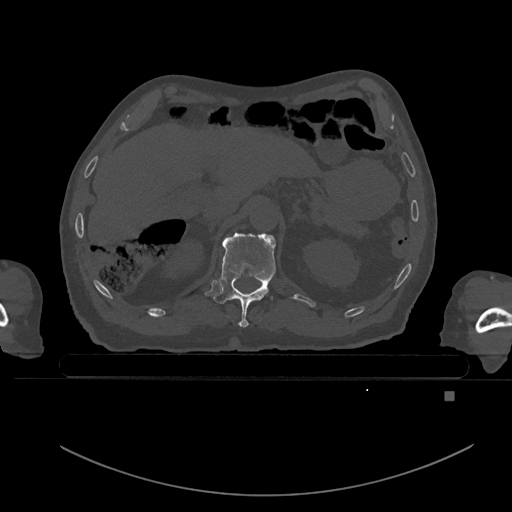
CT including the spine, one axial slice; position 24 of 969 along the scan axis; bone window (W 1800 / L 400 HU); 512 × 512 image matrix, field of view 456 × 456 mm. Patient: male, 82 years. Case-level facts recorded for this patient, not image findings: primary cancer: prostate; vertebrae with lytic lesions (as recorded): T11, T9, T8, T2.
Outlined on this slice (semi-automatic segmentation, software-assisted and operator-edited):
- T11 vertebra: box from (x=213, y=233) to (x=275, y=328) px